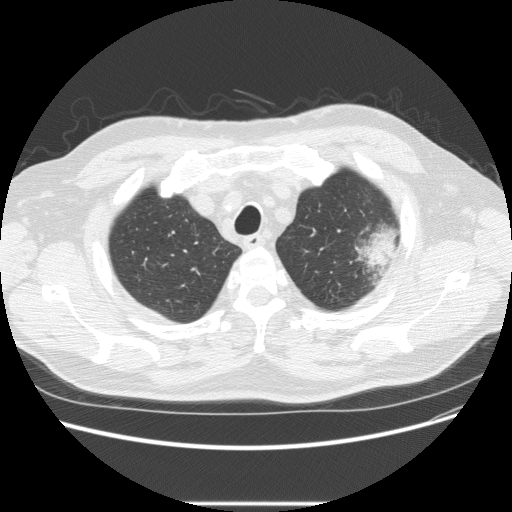
Low-dose screening chest CT, one axial slice; position 192 of 233 along the scan axis; reconstruction kernel STANDARD; 120 kVp; lung window (W 1500 / L -600 HU); 2.5 mm slice thickness; 512 × 512 image matrix, field of view 380 × 380 mm.
Structures marked on this image (outlined manually by an expert reader):
- lesion 1 (tumor, upper lobe of left lung): box from (x=356, y=227) to (x=401, y=272) px